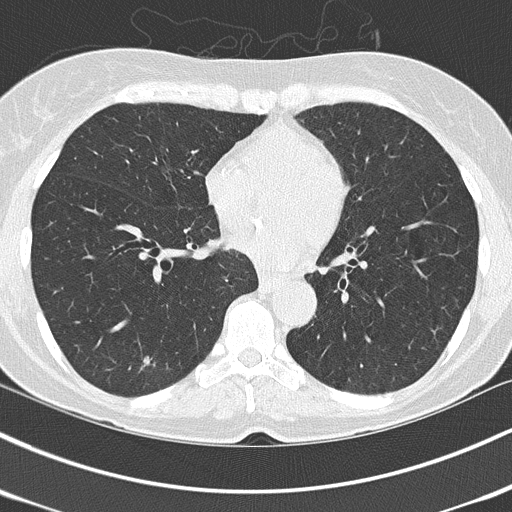
Axial slice from a low-dose chest CT screening exam; third annual screen; lung window (W 1500 / L -600 HU); lung (sharp) reconstruction kernel (B50f); slice 91 of 150 in the series; 512 × 512 image matrix. Female, age 67 years at enrolment. Current smoker at enrolment.
Lesion marked by an expert reader, bounding box (x1, y1, x2, y2) in pixels: (130, 346, 168, 379). The screening reader recorded 3 non-calcified nodules or masses ≥4 mm on this exam (right lower lobe, right lower lobe, left lower lobe); which of them this box marks is not recorded. Participant outcome: lung cancer diagnosed 64 days after this screen — adenocarcinoma, NOS, left lower lobe, poorly differentiated (G3), stage IA (AJCC 6th edition), 25 mm at pathology.